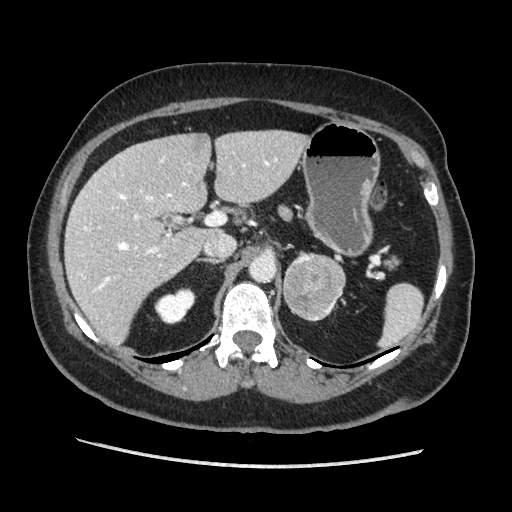
Contrast-enhanced abdominal CT, one axial slice; slice 125 of 203 in the series (ordered by position); soft-tissue window (W 400 / L 40 HU); 512 × 512 image matrix, field of view 360 × 360 mm. Female patient. From the clinical record (not read from this slice): diagnosis: adrenocortical carcinoma; tumour side: left adrenal; tumour size at pathology: 6.5 cm; Ki-67 index: 22 %; stage (as recorded): 2.
Structures marked on this image (semi-automatic segmentation, software-assisted and operator-edited):
- mass: bounding box (x1, y1, x2, y2) in pixels: (284, 252, 347, 321)